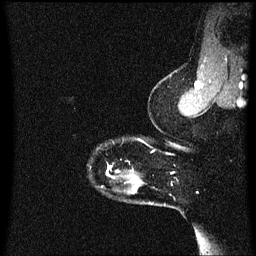
Breast MRI (dynamic contrast-enhanced), one sagittal slice. Position 55 of 60 along the scan axis. Dynamic contrast-enhanced series, image 2 of 3 at this slice position (ordered by acquisition). 1.5 T. TE 4.2 ms, TR 8.4 ms. 2 mm slice thickness. 256 × 256 image matrix, field of view 200 × 200 mm. Female patient, age 33 years.
Outlined on this slice (semi-automatically segmented with operator editing):
- analysis volume of interest (the breast-tissue region the enhancement analysis was run in; not a lesion): bounding box [x1, y1, x2, y2] px = [107, 138, 146, 191]
- tumour enhancement mask (voxels above the 70 % enhancement threshold inside the analysis volume of interest): [107, 166, 113, 177]